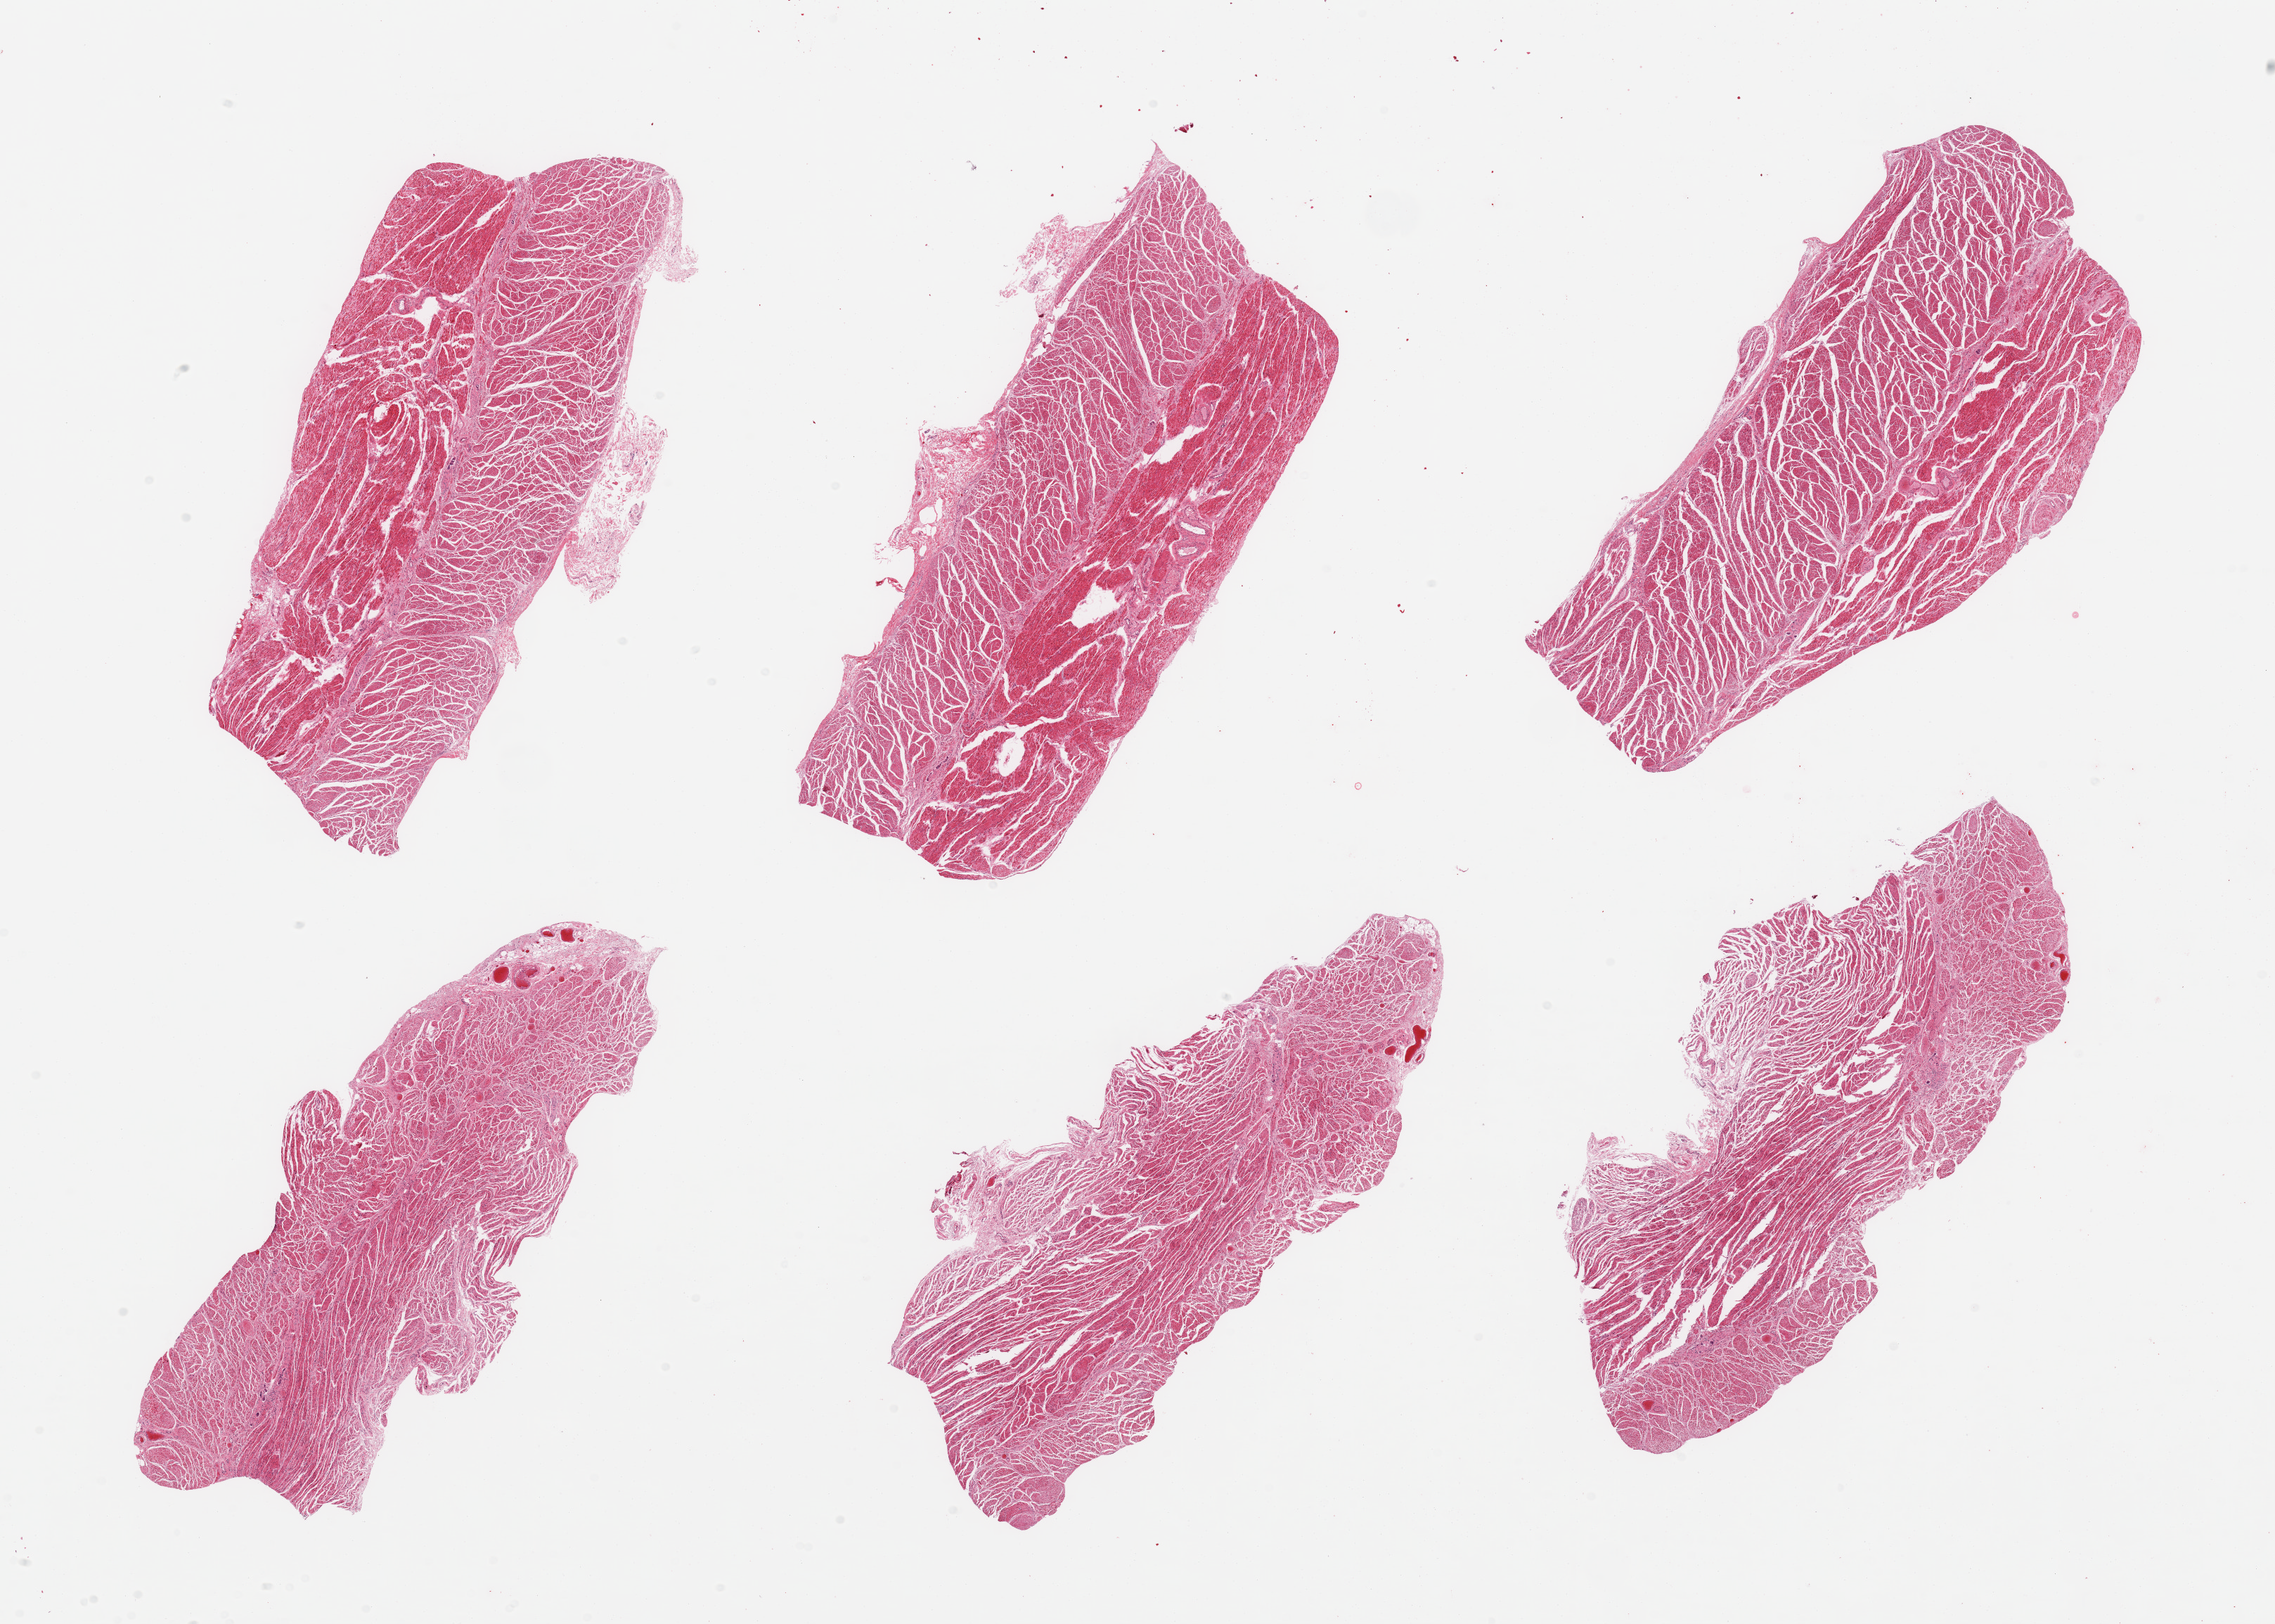
Digitized haematoxylin and eosin-stained section, brightfield, whole scanned area (about 25.6 x 18.3 mm, acquisition: 20x scan) shown as a low-resolution overview, PAXgene-fixed, paraffin-embedded tissue, section of gastroesophageal junction (target tissue), donor tissue sample. Donor sex: male.
Reviewer comment on this tissue sample: 6 pieces; well dissected muscularis.